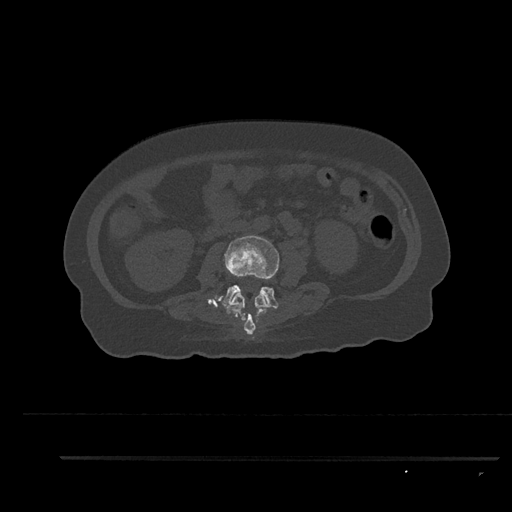
CT including the spine, one axial slice; slice 115 of 797 in the series (ordered by position); reconstruction kernel Br40s/3; bone window (W 1800 / L 400 HU); 0.5 mm slice thickness; 512 × 512 image matrix, field of view 408 × 408 mm. Female patient, age 44 years. From the clinical record (not read from this slice): primary cancer: renal; vertebrae with lytic lesions (as recorded): L1.
Annotated regions visible in this slice (semi-automatically segmented with operator editing):
- L2 vertebra: box from (x=224, y=293) to (x=268, y=335) px
- L3 vertebra: (x=218, y=235)–(x=280, y=309)